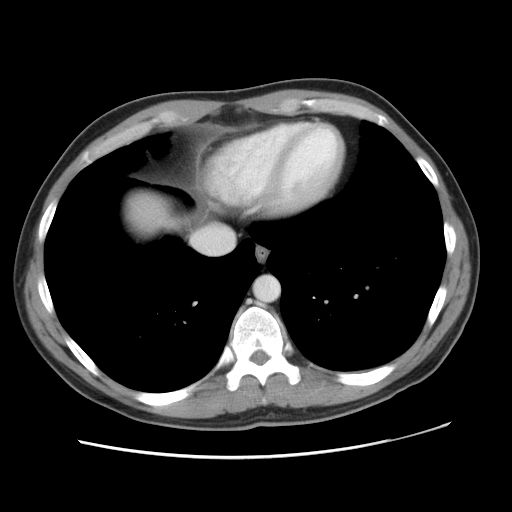
Contrast-enhanced abdominal CT, one axial slice. Slice 45 of 49 in the series (ordered by position). 120 kVp. Intravenous contrast given. Soft-tissue window (W 400 / L 40 HU). 512 × 512 image matrix, field of view 363 × 363 mm. Male patient, age 41 years. From the clinical record (not read from this slice): diagnosis: colorectal cancer liver metastases, imaged before liver resection; multiple liver metastases: yes; largest metastasis: 0.7 cm.
Annotated regions visible in this slice (manually delineated by an expert):
- liver: bounding box <123,192,169,235> (left, top, right, bottom; pixels)
- planned liver remnant (the part of the liver to remain after resection): <136,192,169,219>